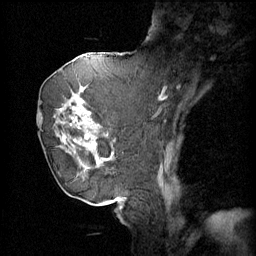
Breast MRI (dynamic contrast-enhanced), one sagittal slice. Position 22 of 60 along the scan axis. 4 images stored at this slice position (order not interpretable as contrast timing). 1.5 T. TE 4.2 ms, TR 11 ms. 256 × 256 image matrix. Female patient, age 72 years.
Structures marked on this image (semi-automatic segmentation, software-assisted and operator-edited):
- analysis volume of interest (the breast-tissue region the enhancement analysis was run in; not a lesion): bounding box (x1, y1, x2, y2) in pixels: (44, 68, 109, 163)
- tumour enhancement mask (voxels above the 70 % enhancement threshold inside the analysis volume of interest): (46, 72, 109, 163)